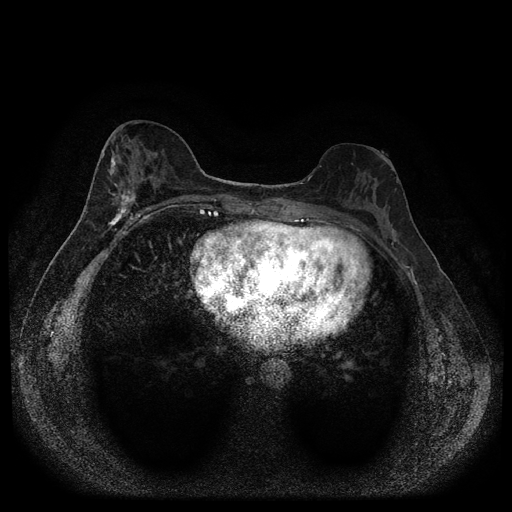
Breast MRI (dynamic contrast-enhanced, multi-phase), one axial slice. Position 43 of 116 along the scan axis. Dynamic contrast-enhanced series, time point 2 of 5 at this slice position (early post-contrast). 1.5 T. TE 2.7 ms, TR 5.4 ms. 2 mm slice thickness. 512 × 512 image matrix, field of view 330 × 330 mm. Patient: female, 49 years.
Outlined on this slice (semi-automatically segmented with operator editing):
- breast lesion (labelled 'tumour' in the annotation; benign lesions carry a separate 'benign' label): bounding box <106,155,138,230> (left, top, right, bottom; pixels)